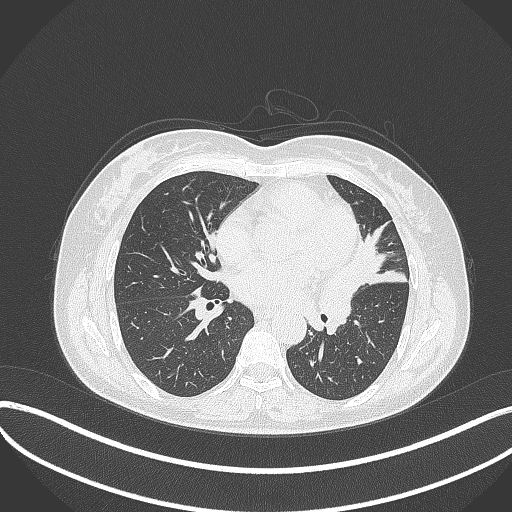
Chest CT, one axial slice; reconstruction kernel B70f; 120 kVp; lung window (W 1500 / L -600 HU); 1 mm slice thickness; 512 × 512 image matrix, field of view 400 × 400 mm. Female patient, age 54 years. Case-level facts recorded for this patient, not image findings: clinical TNM (as recorded): T2a N1 M0.
Annotated regions visible in this slice (rectangle marked by the reading radiologist):
- lung tumour (recorded histology: small cell carcinoma): box from (x=318, y=261) to (x=362, y=326) px